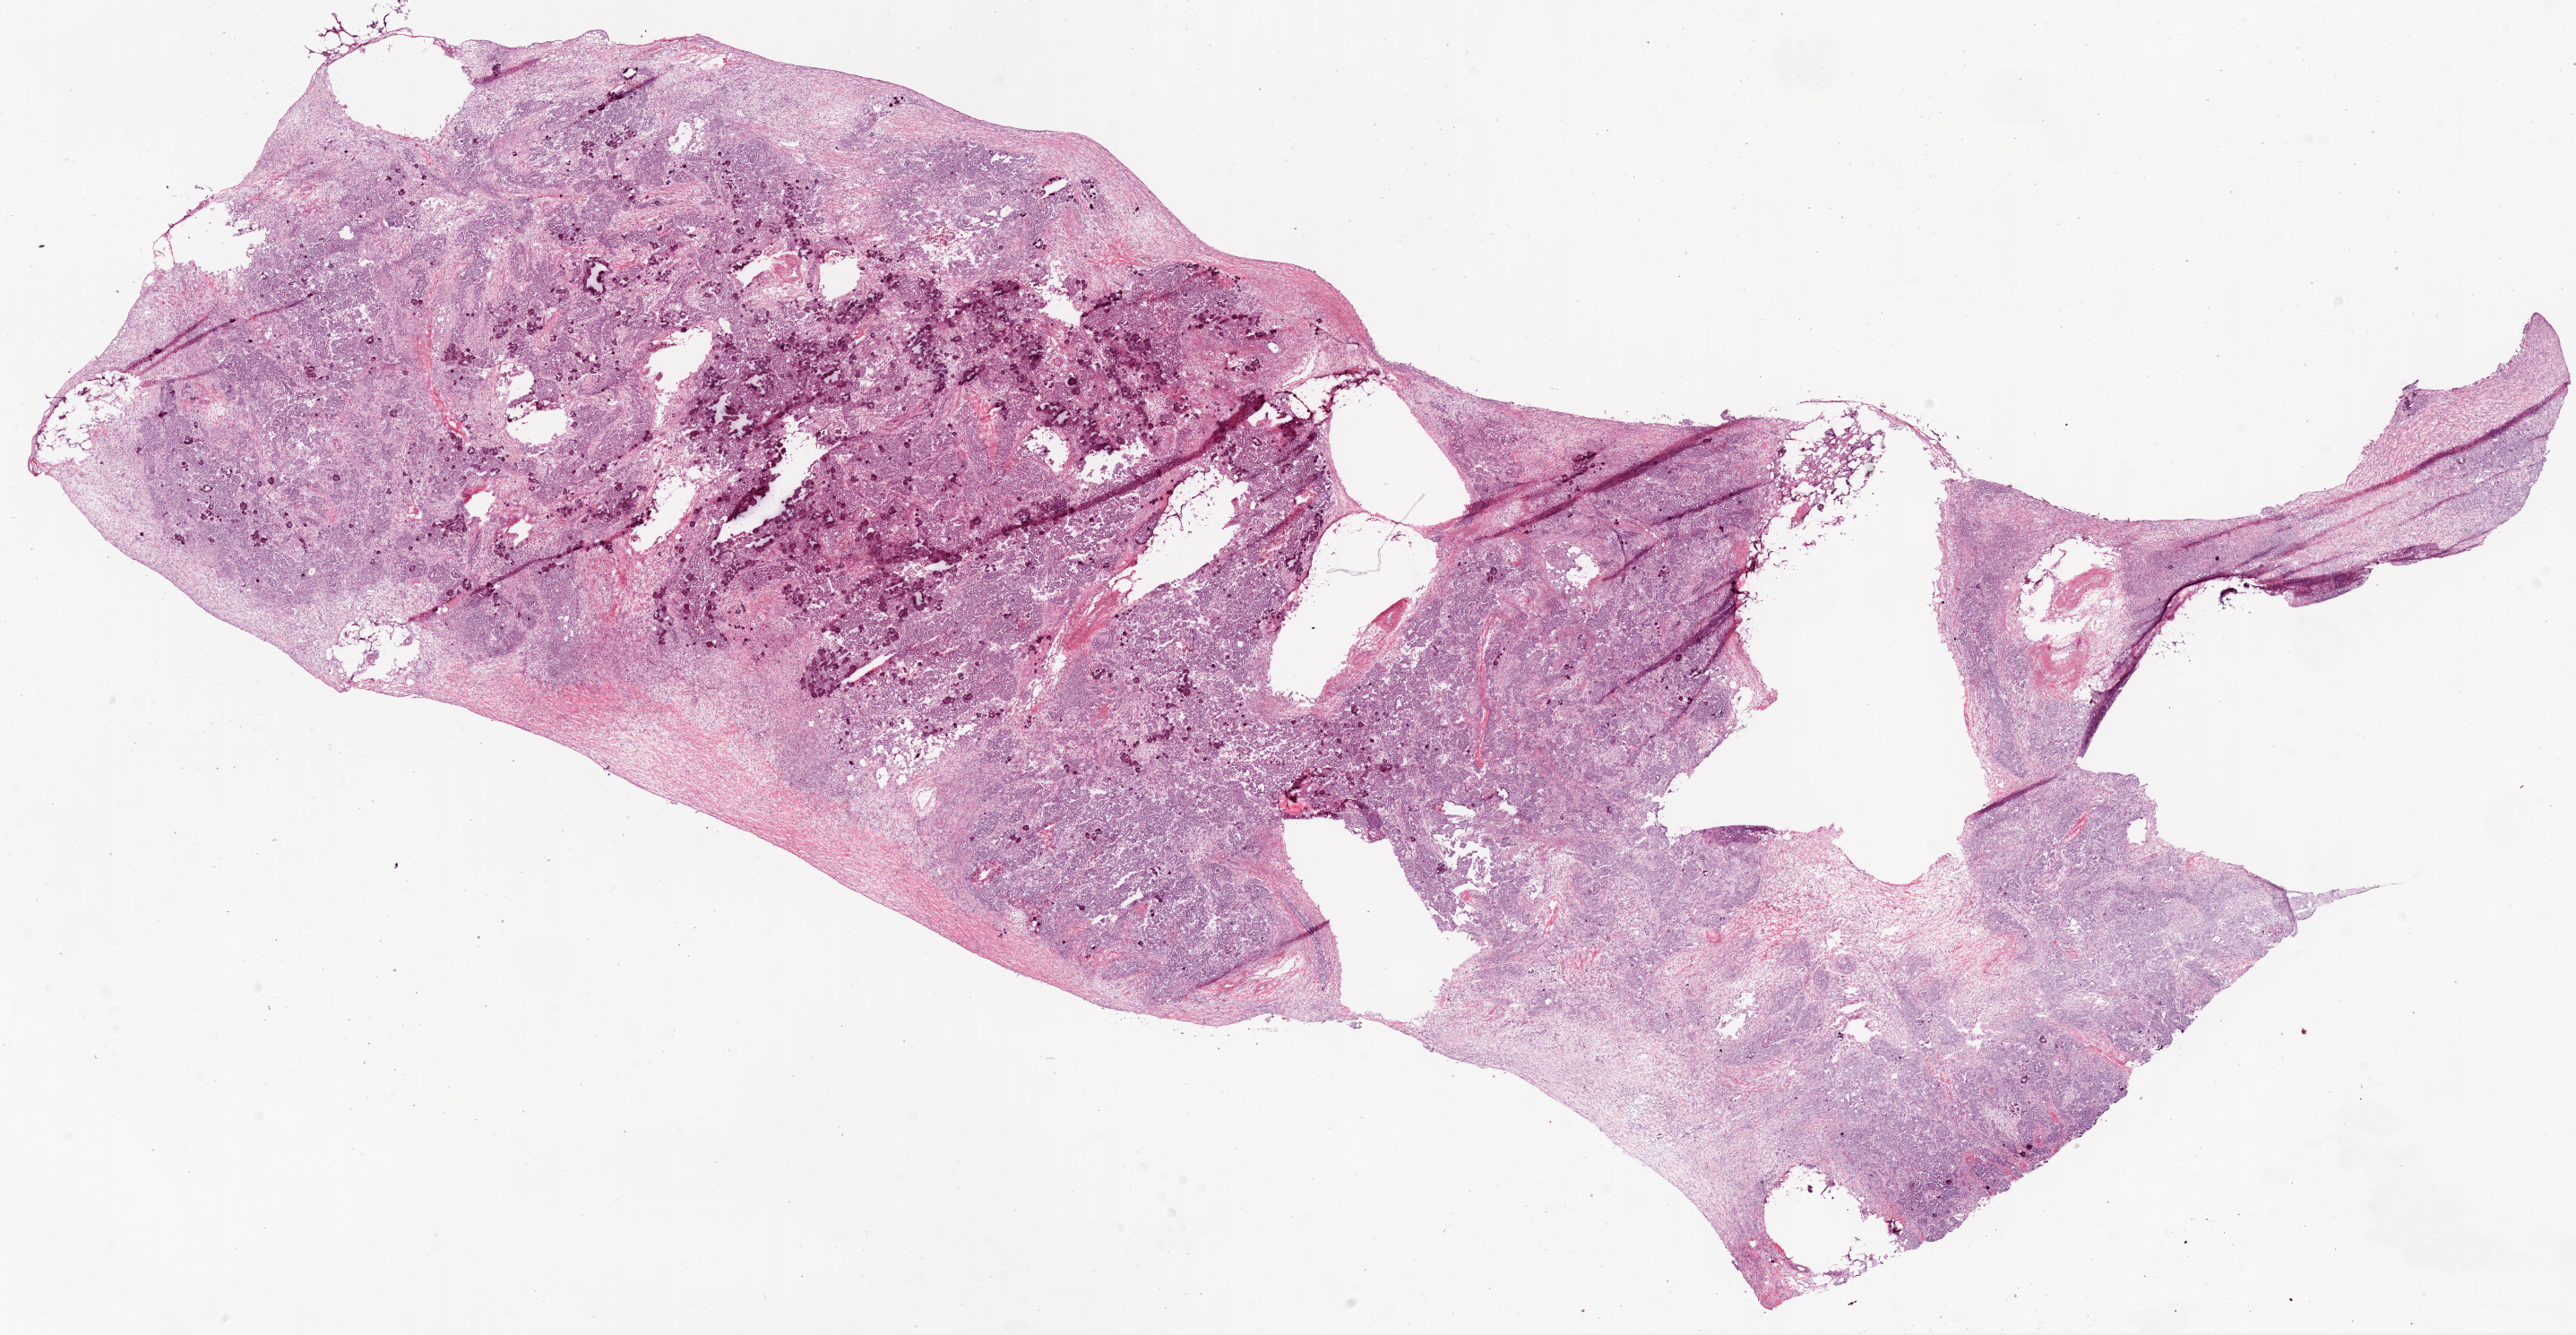
Hematoxylin and eosin (H&E) stained whole-slide image — low-resolution overview of the scanned area, about 23.1 x 12.0 mm (from a 20x scan). Frozen section. Sample: primary tumour, ovary. Female, age 67 years at initial diagnosis. Pathologist review of this section (percent, as recorded): tumour cells 85%, tumour nuclei 95%.
Pathologic diagnosis: Serous cystadenocarcinoma, NOS.